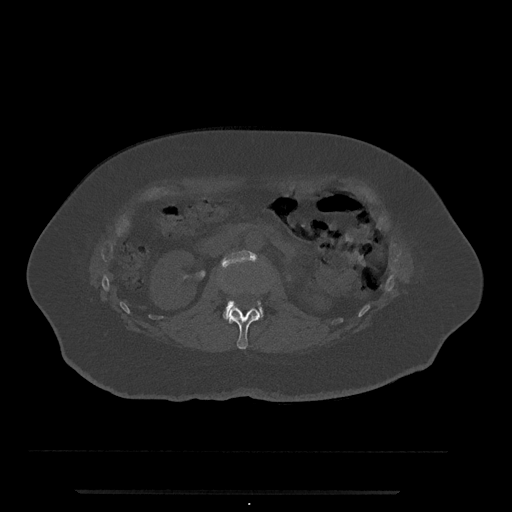
CT including the spine, one axial slice; position 73 of 797 along the scan axis; reconstruction kernel Br40s/3; 120 kVp; bone window (W 1800 / L 400 HU); 512 × 512 image matrix, field of view 440 × 440 mm. Patient: female, 51 years. Case-level facts recorded for this patient, not image findings: primary cancer: neuro; vertebrae with lytic lesions (as recorded): T8.
Outlined on this slice (semi-automatic segmentation, software-assisted and operator-edited):
- L1 vertebra: bounding box [x1, y1, x2, y2] px = [223, 307, 261, 350]
- L2 vertebra: [222, 250, 264, 318]